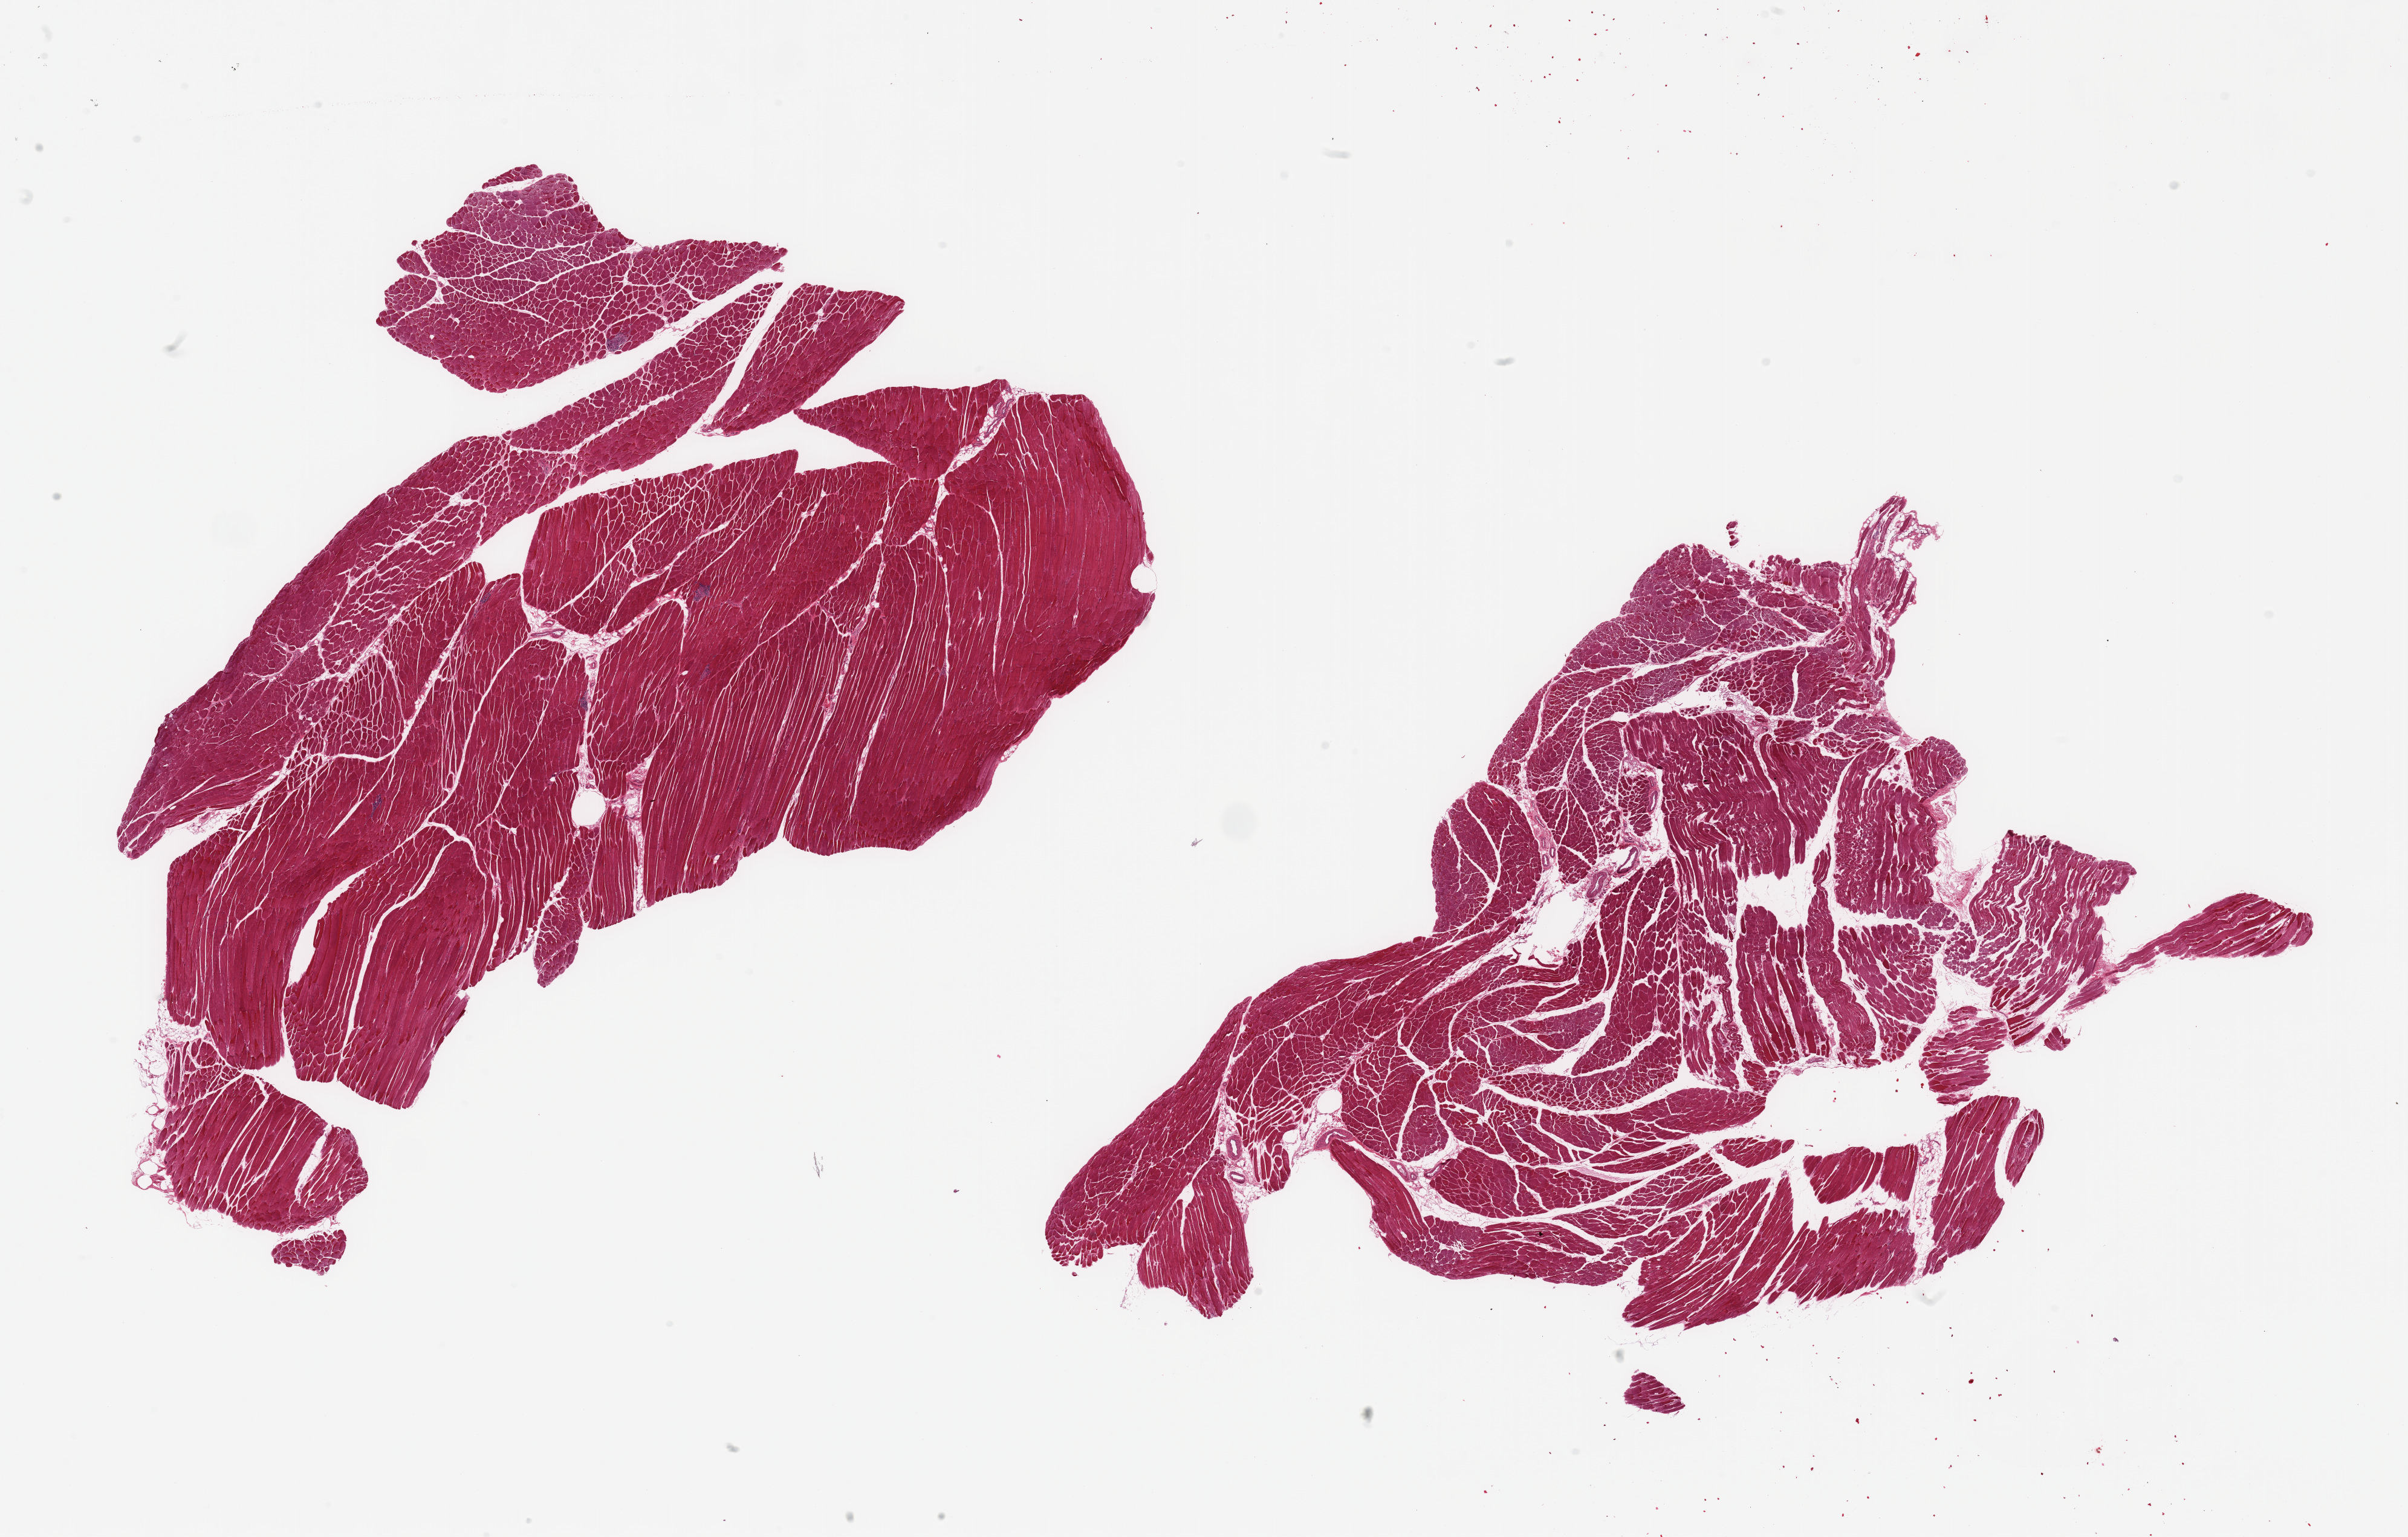
Haematoxylin and eosin whole-slide image, brightfield, whole scanned area (about 31.5 x 20.1 mm, acquisition: 20x scan) shown as a low-resolution overview; PAXgene-fixed, paraffin-embedded tissue; sampled site (target tissue): skeletal muscle; tissue donor sample. Male donor.
Review note (as recorded): 2 pieces, minimal fat.